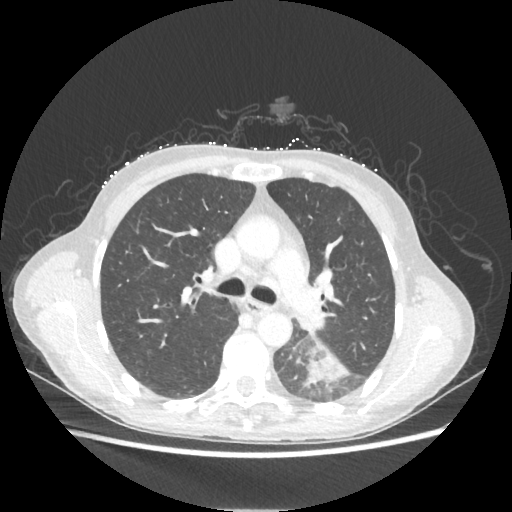
Chest CT, one axial slice; slice 140 of 221 in the series (ordered by position); reconstruction kernel STANDARD; lung window (W 1500 / L -600 HU); 512 × 512 image matrix. Female patient, age 53 years. Case-level facts recorded for this patient, not image findings: clinical TNM (as recorded): T3 N0 M0.
Structures marked on this image (rectangle marked by the reading radiologist):
- lung tumour (recorded histology: adenocarcinoma): bounding box [x1, y1, x2, y2] px = [305, 344, 347, 386]